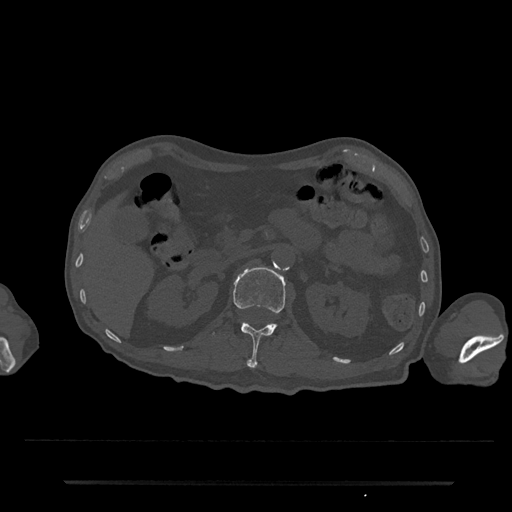
CT including the spine, one axial slice; reconstruction kernel Br40s/3; bone window (W 1800 / L 400 HU); 0.5 mm slice thickness; 512 × 512 image matrix, field of view 427 × 427 mm. Male patient, age 74 years. From the clinical record (not read from this slice): primary cancer: prostate.
Structures marked on this image (semi-automatically segmented with operator editing):
- L1 vertebra: bounding box (x1, y1, x2, y2) in pixels: (211, 266, 285, 368)